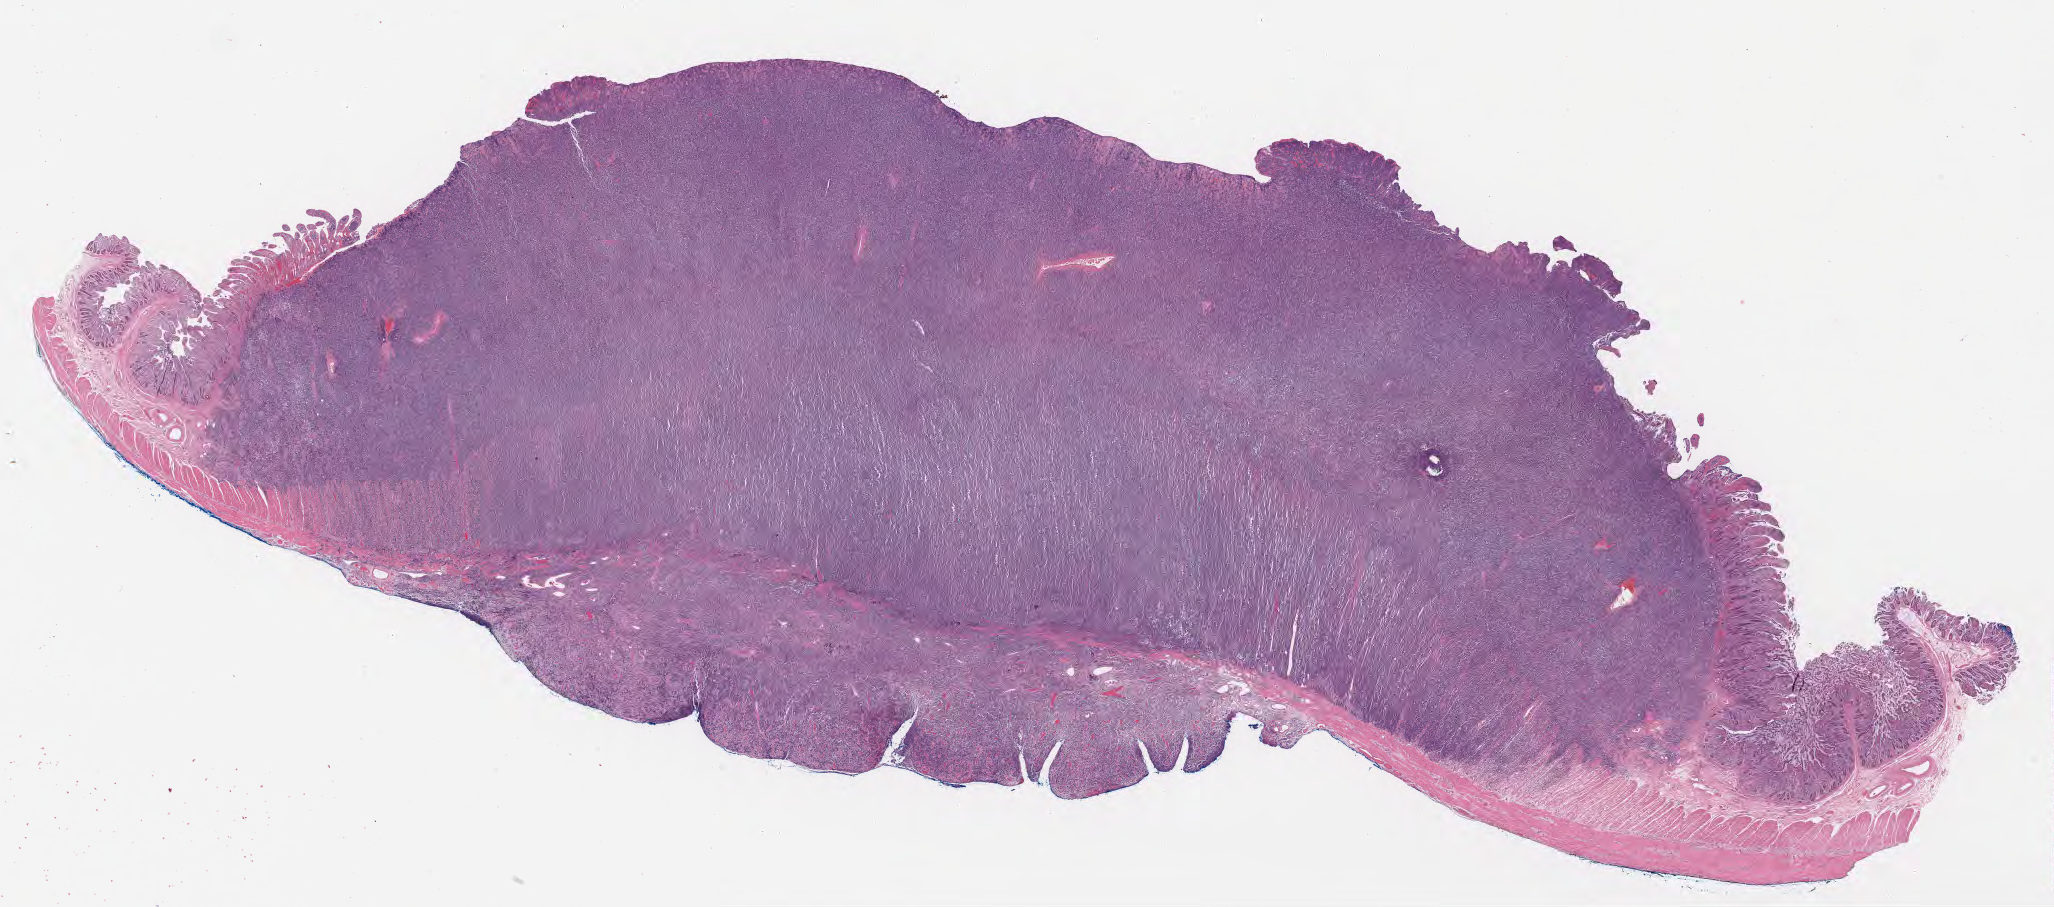
Digitized hematoxylin and eosin (H&E)-stained section, low-resolution overview of the scanned area, about 33.2 x 14.7 mm; tumor tissue; site: small intestine. Male, age 6 years at initial diagnosis.
Histologic diagnosis: Burkitt lymphoma, NOS.